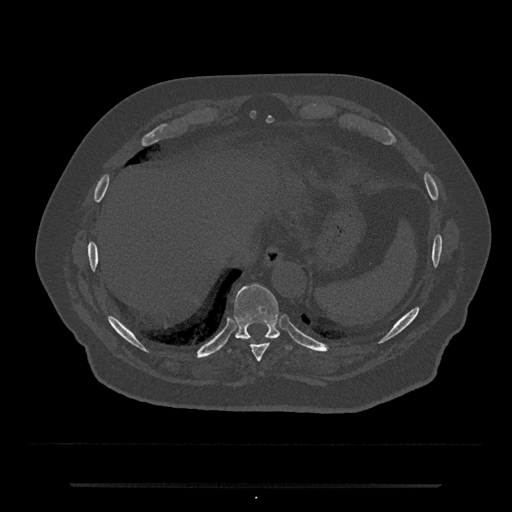
CT including the spine, one axial slice. Slice 730 of 797 in the series (ordered by position). Bone window (W 1800 / L 400 HU). 512 × 512 image matrix, field of view 434 × 434 mm. Male patient, age 80 years. From the clinical record (not read from this slice): primary cancer: prostate.
Structures marked on this image (semi-automatic segmentation, software-assisted and operator-edited):
- T10 vertebra: bounding box (x1, y1, x2, y2) in pixels: (229, 284, 292, 352)
- T9 vertebra: (243, 338, 274, 362)